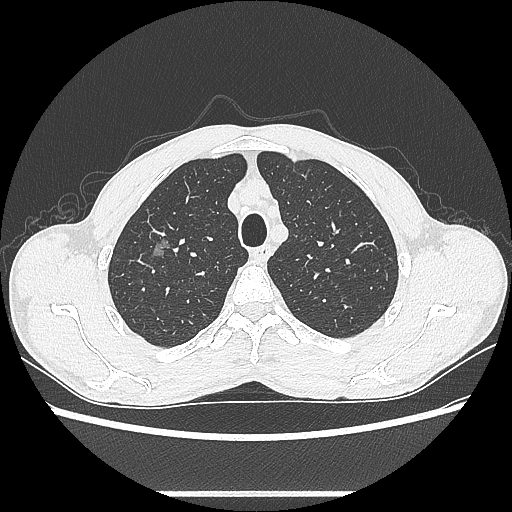
Chest CT, one axial slice. Position 478 of 601 along the scan axis. 100 kVp. Lung window (W 1500 / L -600 HU). 512 × 512 image matrix, field of view 357 × 357 mm. Male patient, age 54 years. From the clinical record (not read from this slice): clinical TNM (as recorded): T1a N0 M0.
Outlined on this slice (rectangle marked by the reading radiologist):
- lung tumour (recorded histology: adenocarcinoma): bounding box (x1, y1, x2, y2) in pixels: (142, 227, 178, 269)